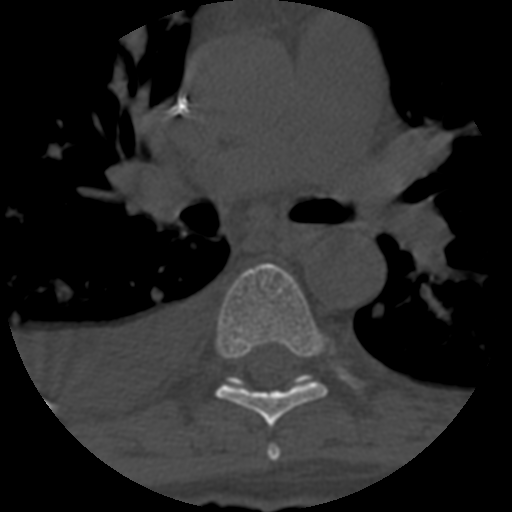
CT including the spine, one axial slice. Slice 433 of 708 in the series (ordered by position). Reconstruction kernel STANDARD. 120 kVp. One of 3 acquisitions stored at this slice position. Bone window (W 1800 / L 400 HU). 1.25 mm slice thickness. 512 × 512 image matrix. Patient age 55 years. Case-level facts recorded for this patient, not image findings: primary cancer: colon.
Structures marked on this image (semi-automatic segmentation, software-assisted and operator-edited):
- T5 vertebra: bounding box (x1, y1, x2, y2) in pixels: (267, 445, 281, 461)
- T6 vertebra: (216, 263, 328, 428)